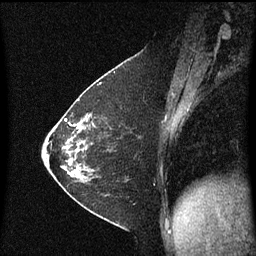
Breast MRI (dynamic contrast-enhanced), one sagittal slice; position 26 of 60 along the scan axis; dynamic contrast-enhanced series, image 2 of 3 at this slice position (ordered by acquisition); 1.5 T; TE 4.2 ms, TR 8.4 ms; 2 mm slice thickness; 256 × 256 image matrix, field of view 200 × 200 mm. Female patient, age 36 years. From the clinical record (not read from this slice): setting: breast cancer imaged before/during neoadjuvant chemotherapy; receptor status: HR-positive, HER2-negative.
Outlined on this slice (semi-automatic segmentation, software-assisted and operator-edited):
- analysis volume of interest (the breast-tissue region the enhancement analysis was run in; not a lesion): bounding box <72,116,109,183> (left, top, right, bottom; pixels)
- tumour enhancement mask (voxels above the 70 % enhancement threshold inside the analysis volume of interest): <72,116,91,175>